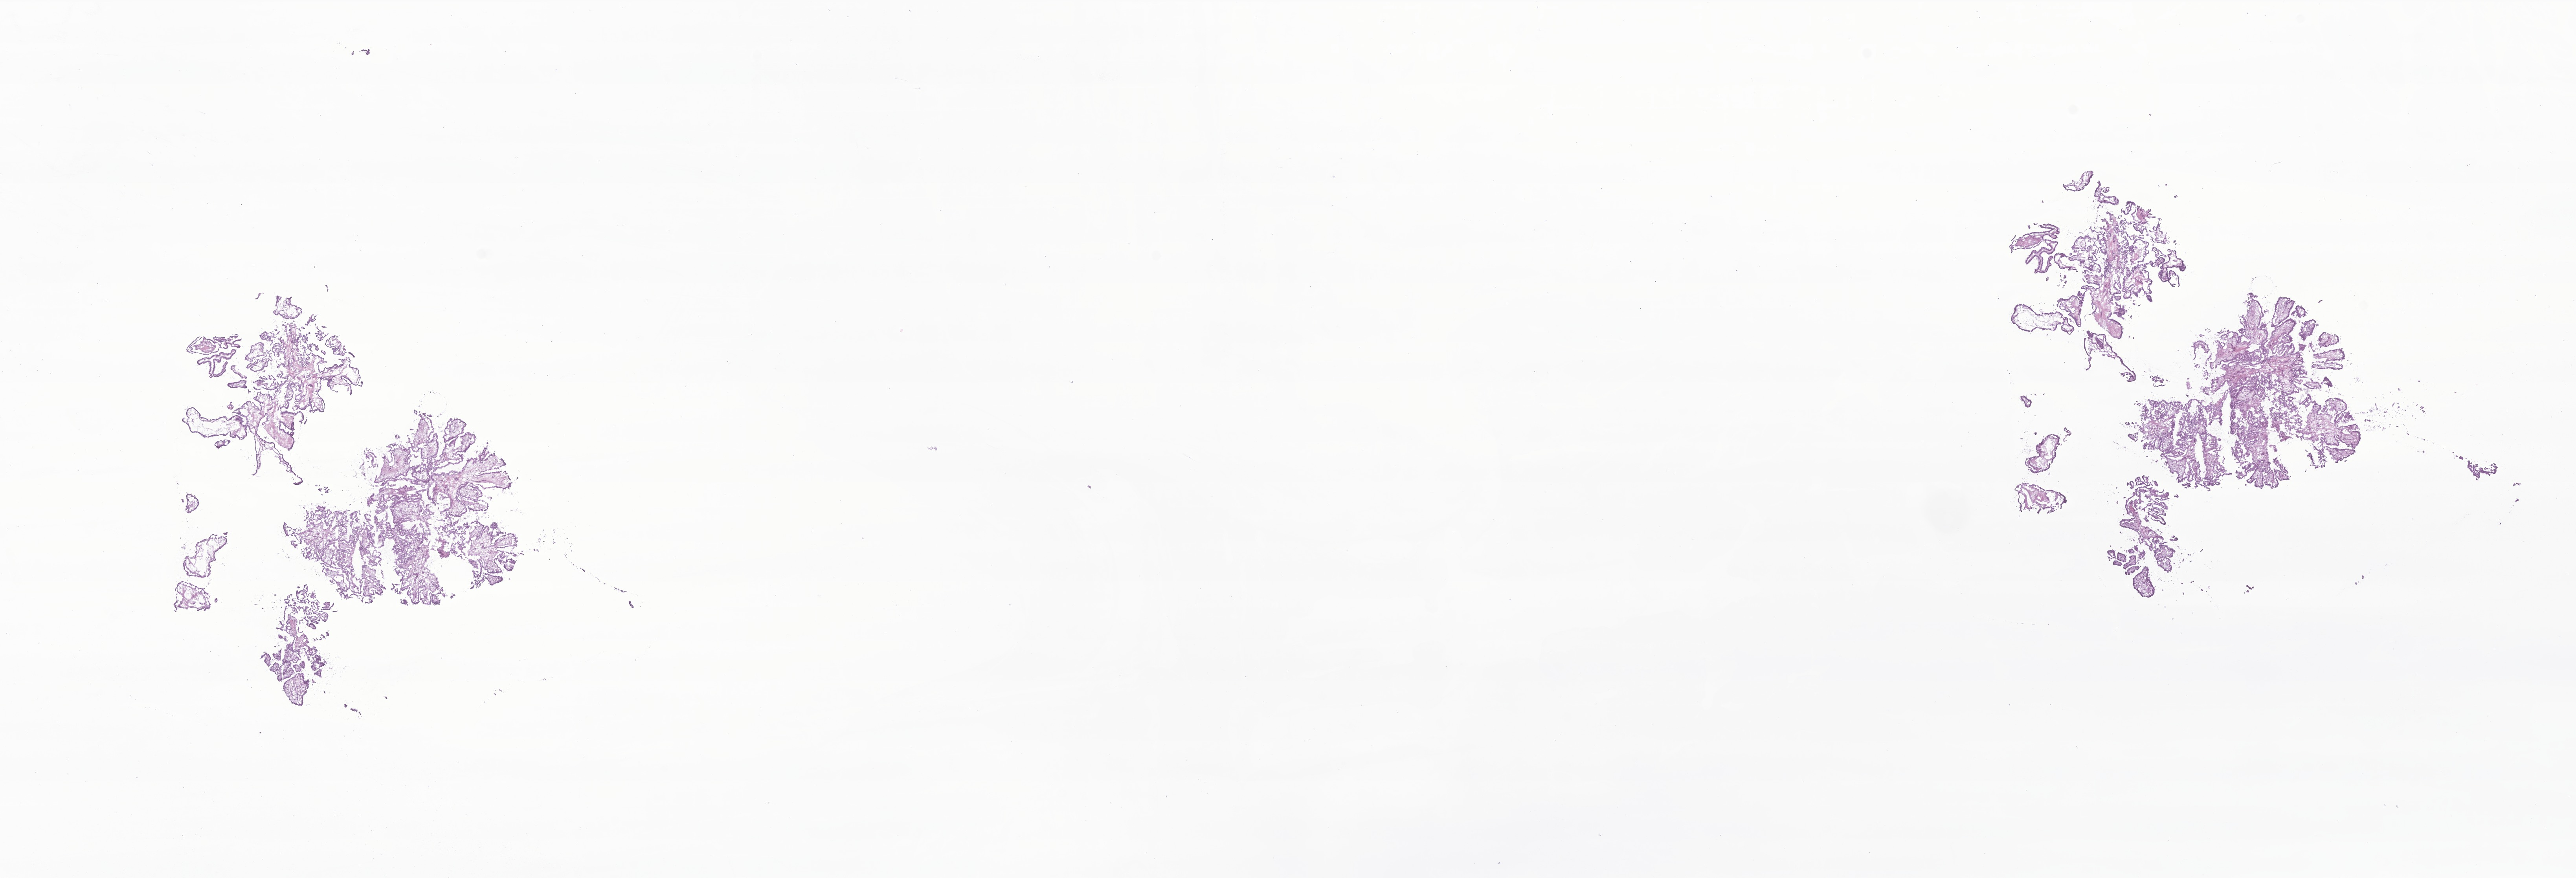
H&E whole-slide image of tumor tissue from the thyroid — whole scanned area (about 27.6 x 9.4 mm) shown as a low-resolution overview. Frozen section (OCT-embedded). Patient male; age 211 months (17 years 7 months).
Recorded diagnosis: Papillary carcinoma, NOS.